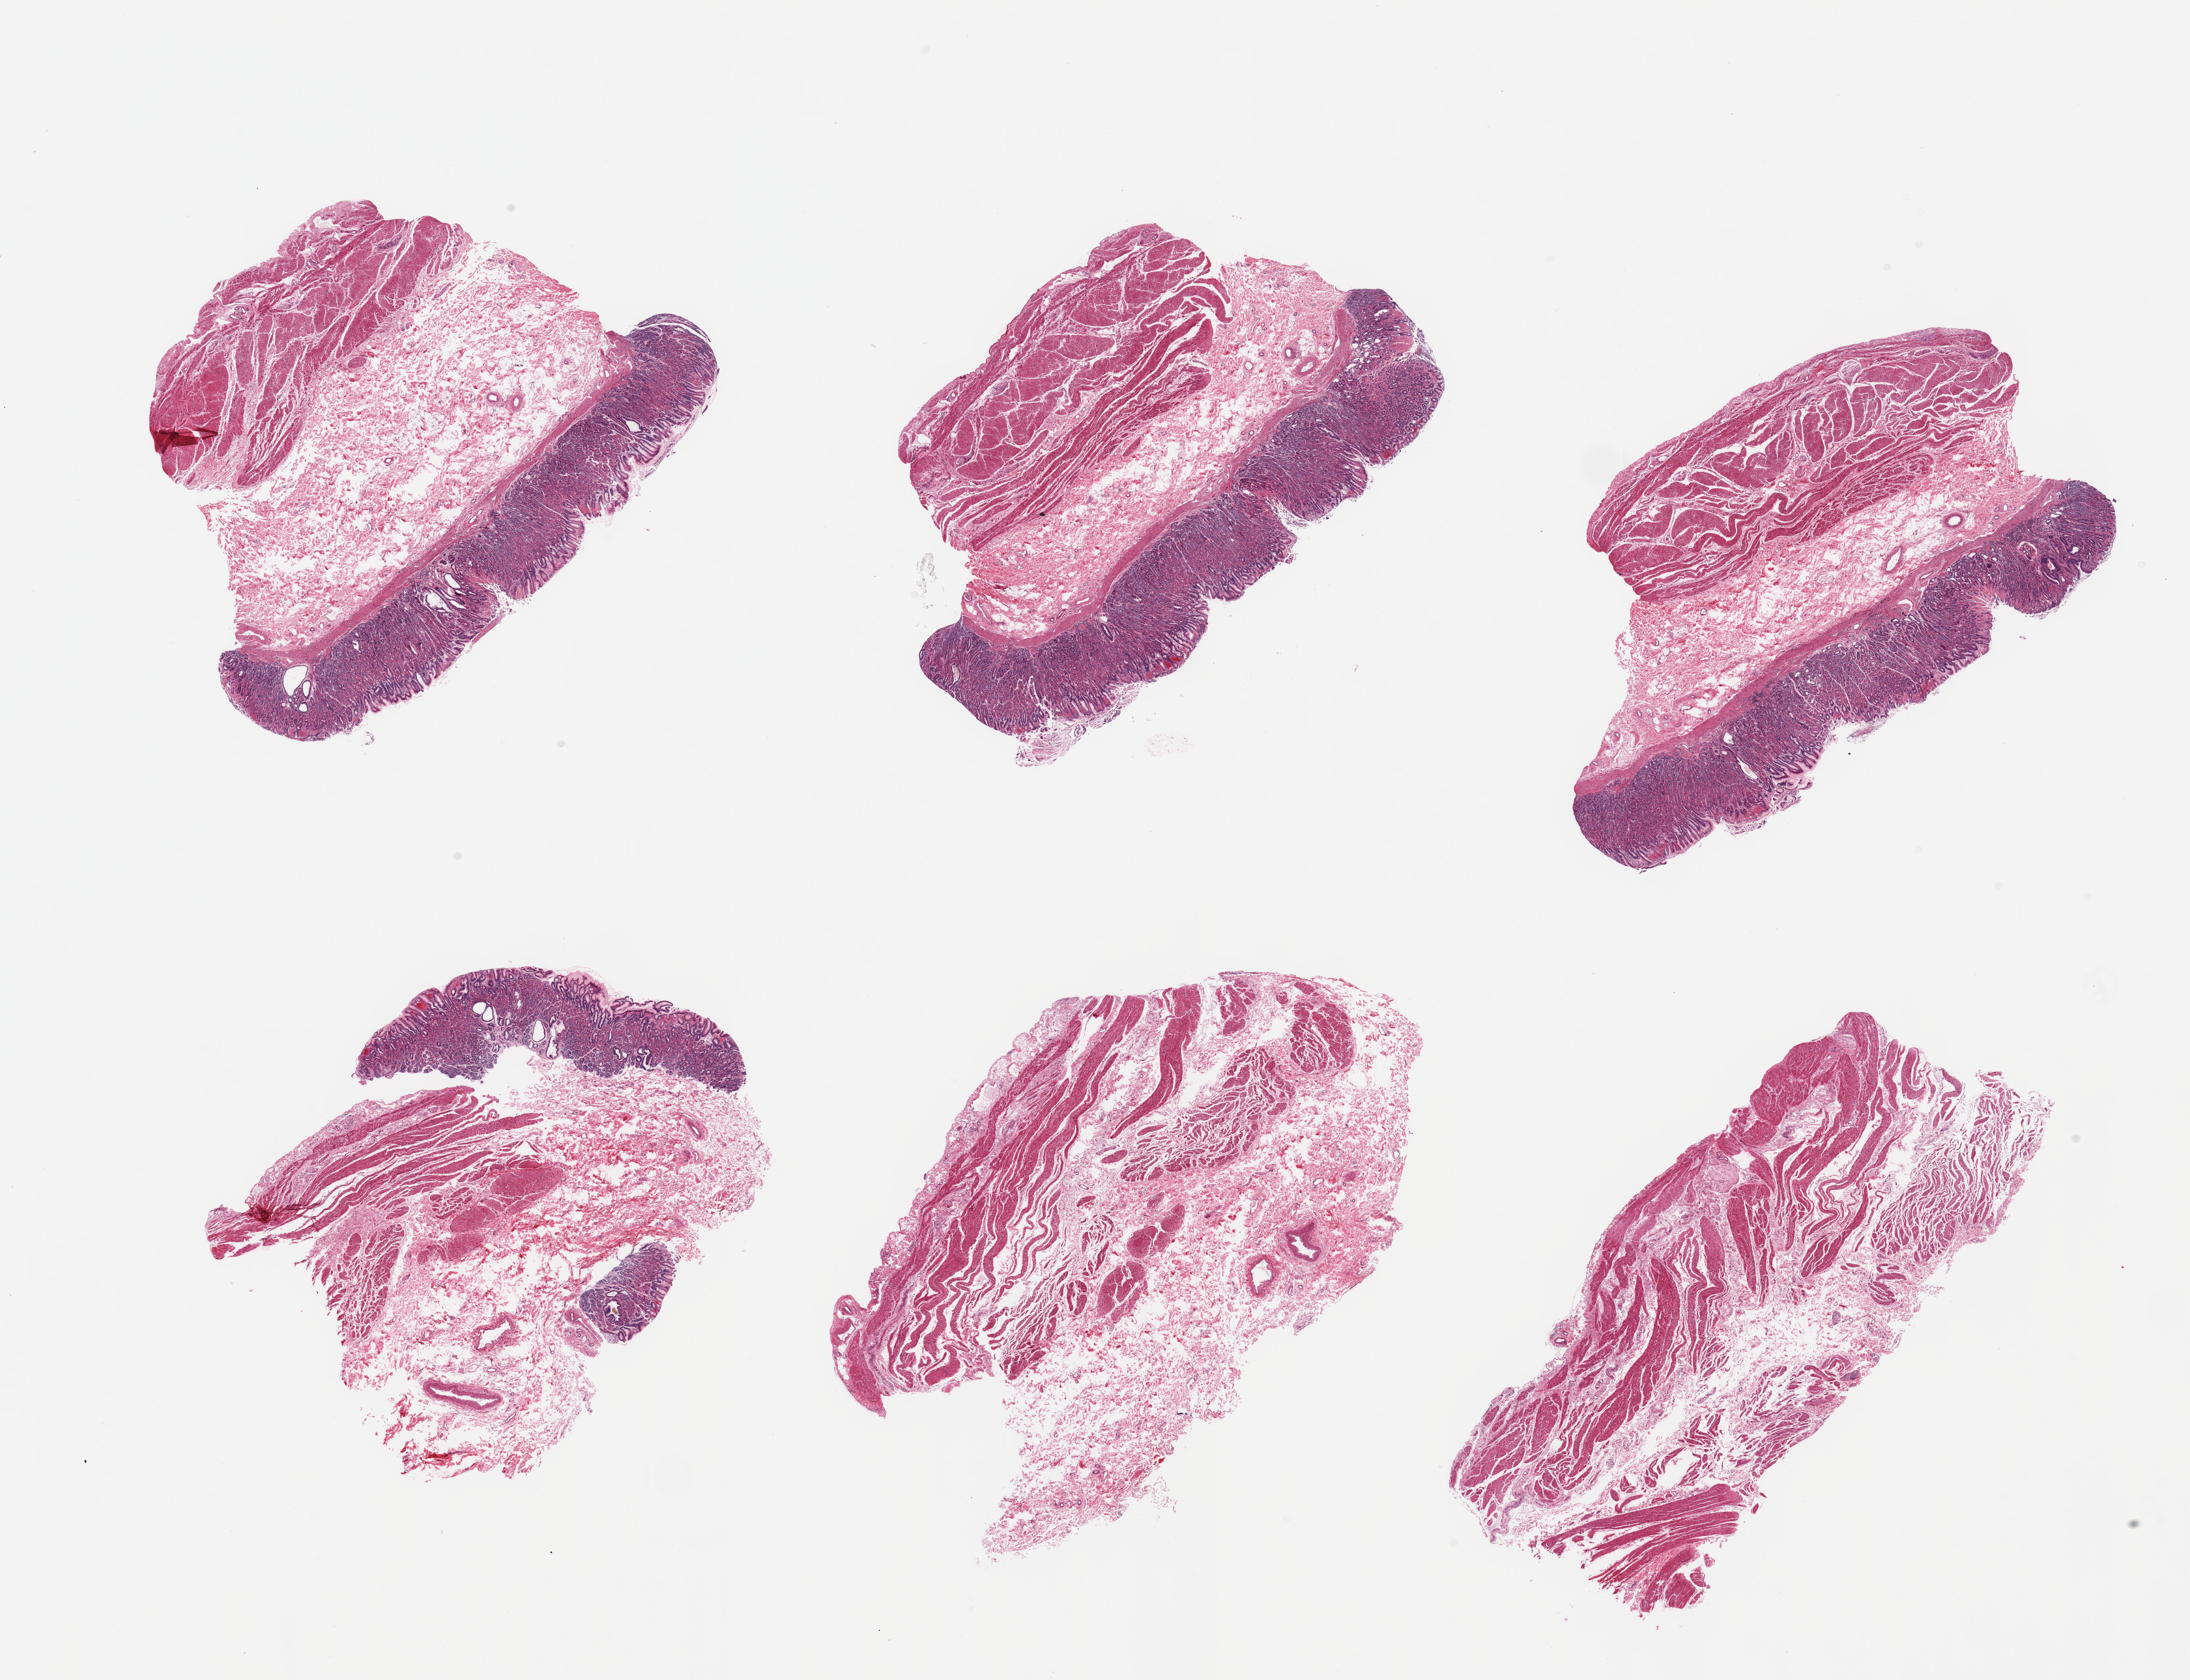
Haematoxylin and eosin whole-slide image, brightfield, low-resolution overview of the scanned area, about 26.6 x 20.4 mm; PAXgene-fixed paraffin-embedded (PFPE) section; sampled site (target tissue): stomach; tissue donor sample. Donor sex: male.
Pathologist's review note for this sample: 6 pieces; 2 pieces have no mucosa; microcystic glands in well preserved mucosa.